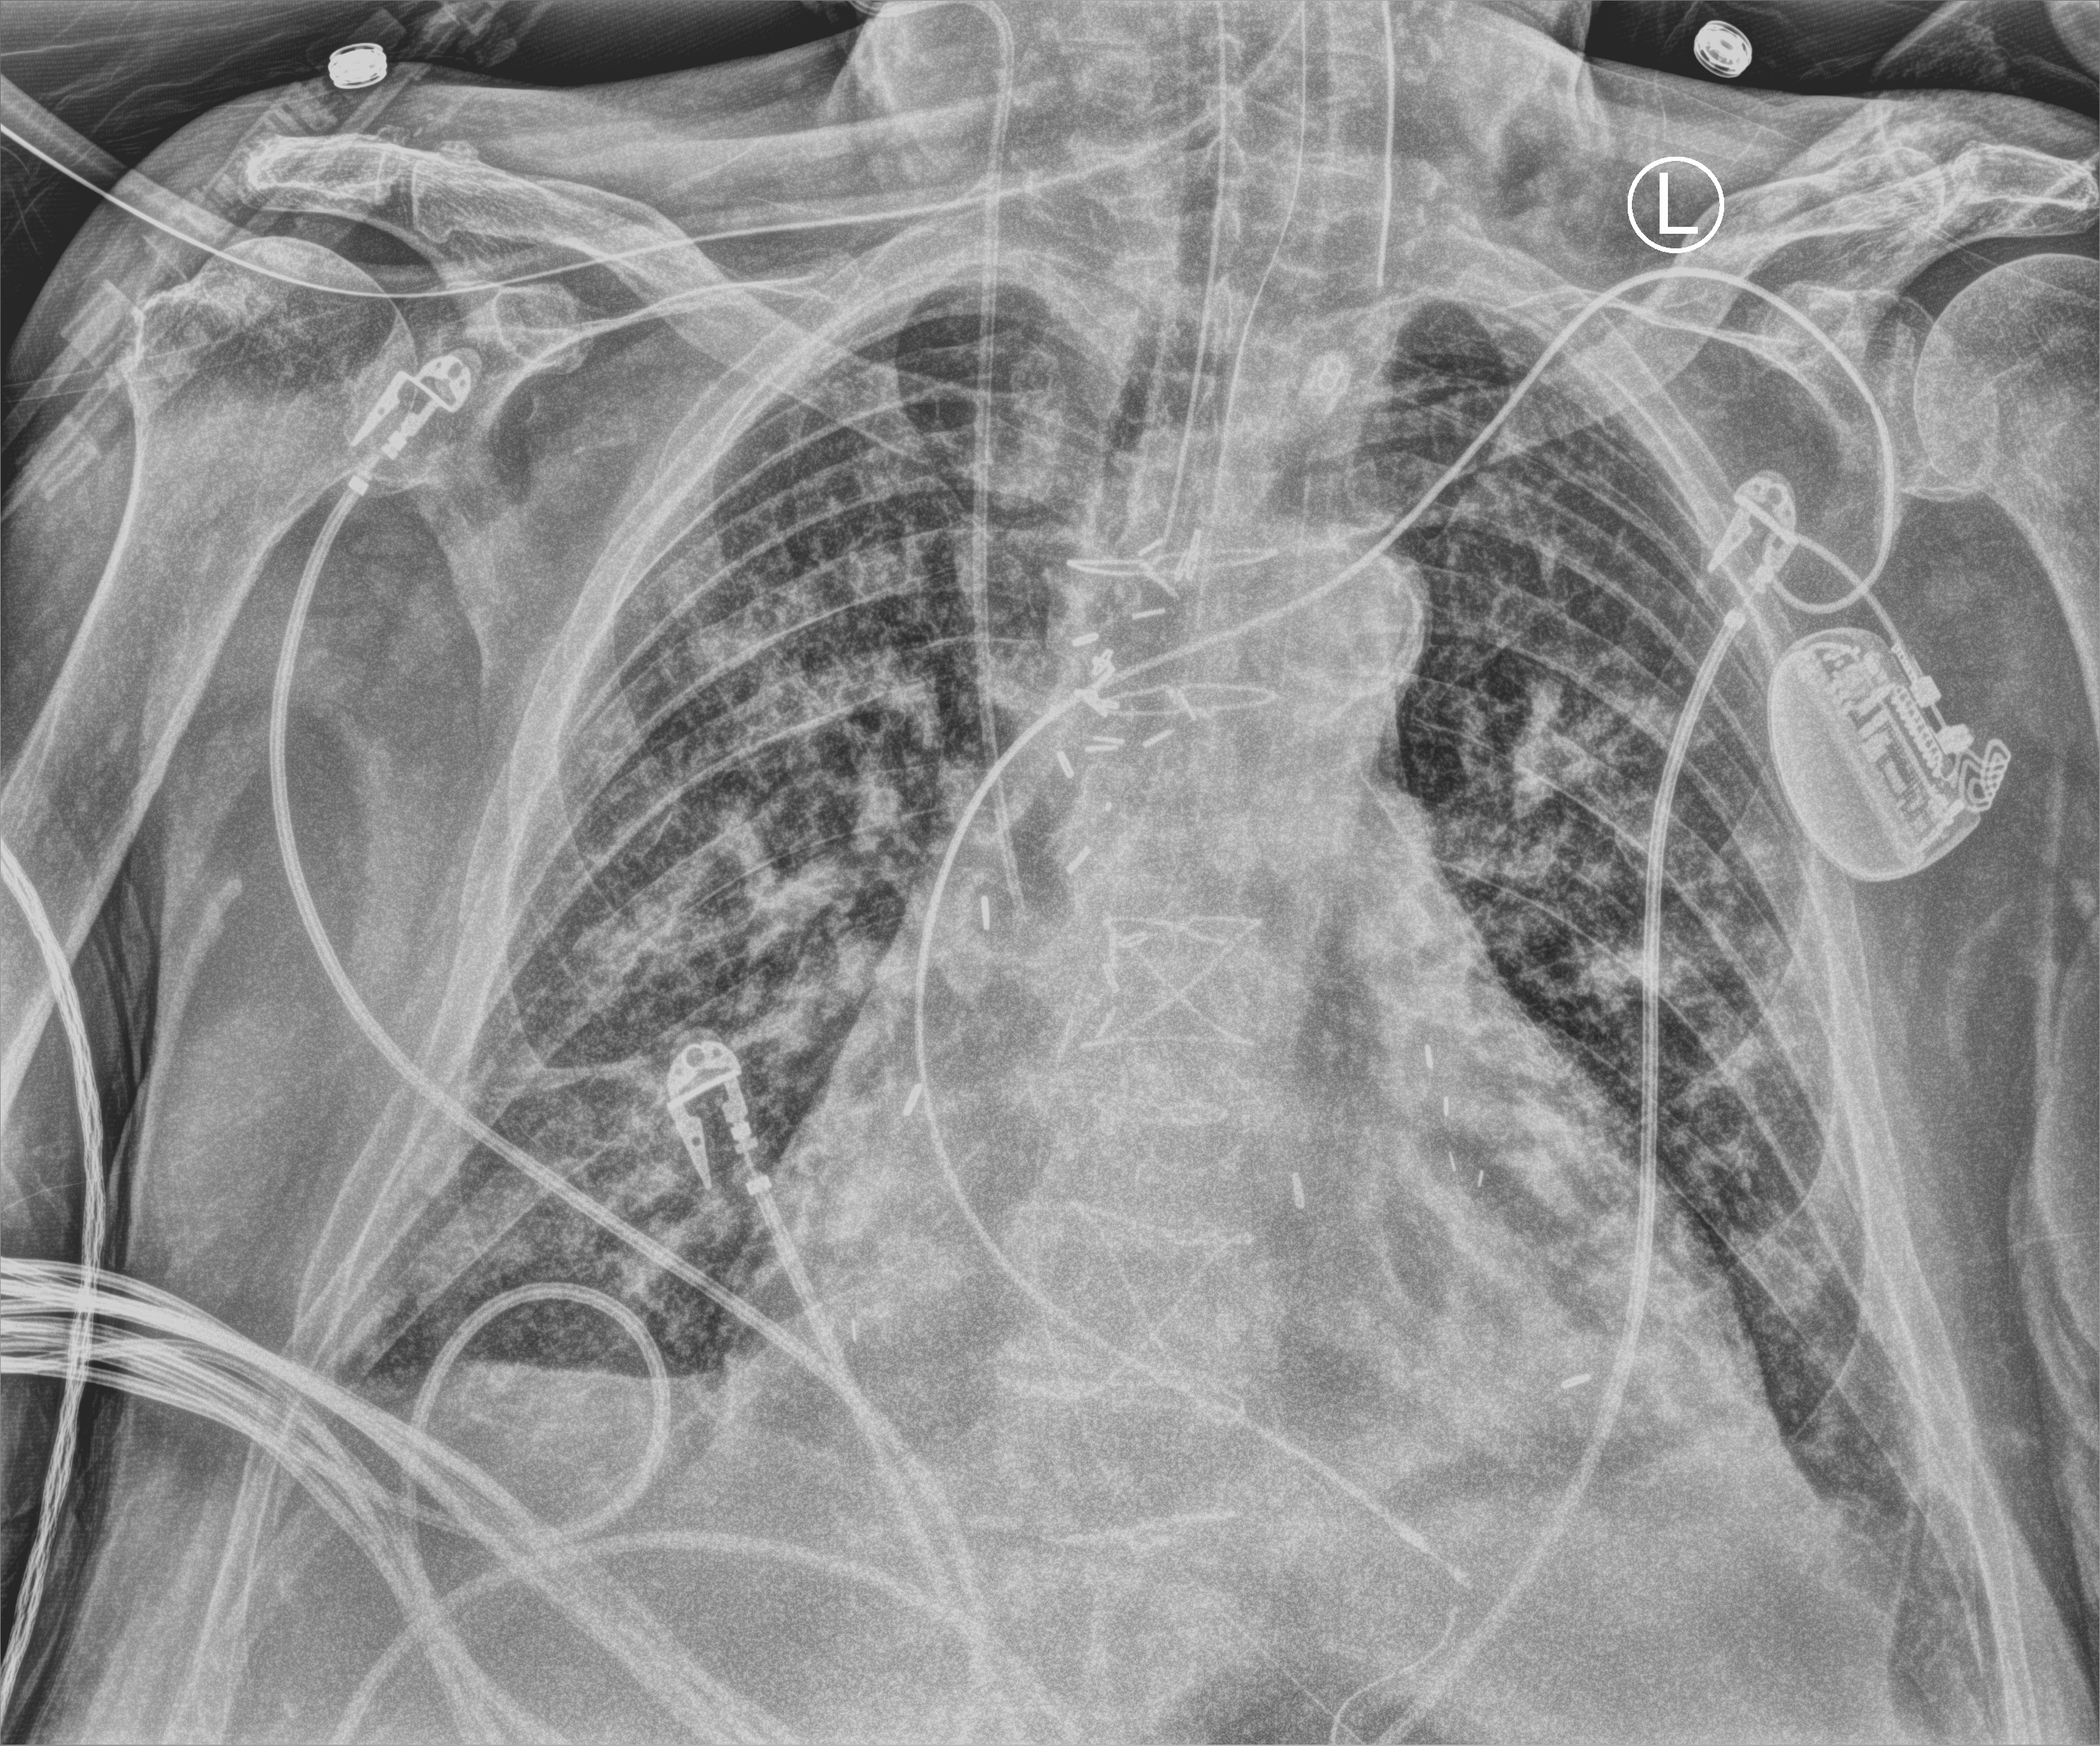
Bedside chest radiograph (computed radiography); anteroposterior (AP) projection. Patient hospitalised with COVID-19; male, aged 75–90 years.
Admission-level facts for this patient (not findings on this image; timing relative to this image not recorded): admitted to intensive care during this hospital stay: yes; mechanically ventilated during this hospital stay: yes.